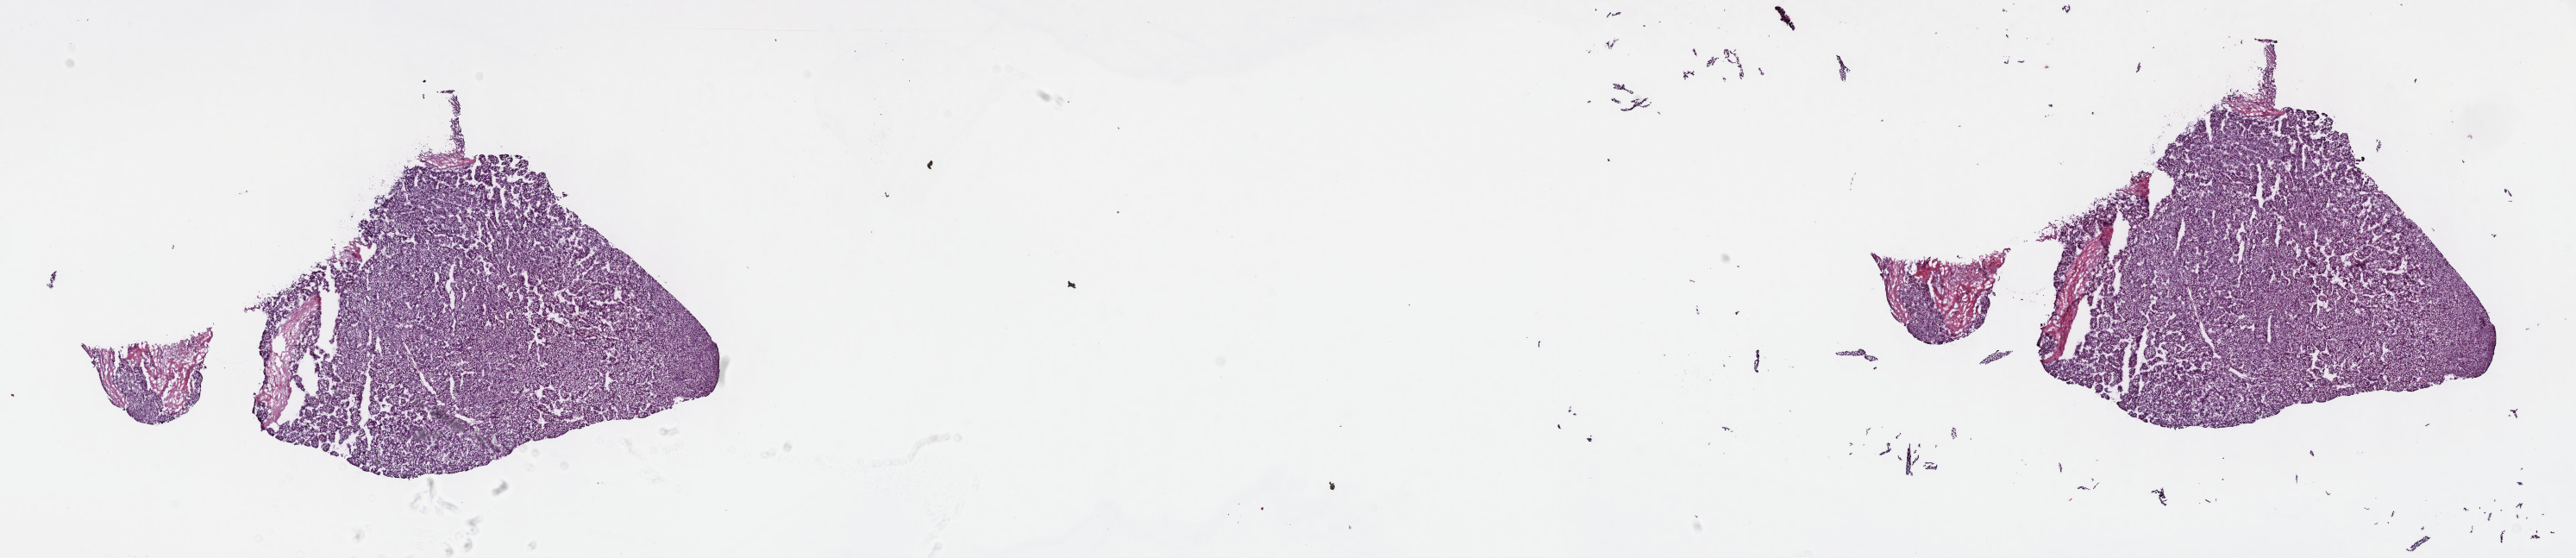
Digitized Hematoxylin and eosin (H&E) stained tissue section (whole slide) — low-resolution overview of the scanned area, about 24.2 x 5.2 mm (from a 40x scan), frozen section, sample: recurrent tumour, liver. Male patient; age at initial diagnosis 65 years. Pathologist review of this section (percent, as recorded): tumour cells 80%, tumour nuclei 80%, normal cells 0%, stromal cells 20%, necrosis 0%. Inflammatory infiltration, as recorded: lymphocyte infiltration 3%, monocyte infiltration 1%, neutrophil infiltration 2%.
• this section: recurrent tumour
• patient diagnosis: Hepatocellular carcinoma, NOS